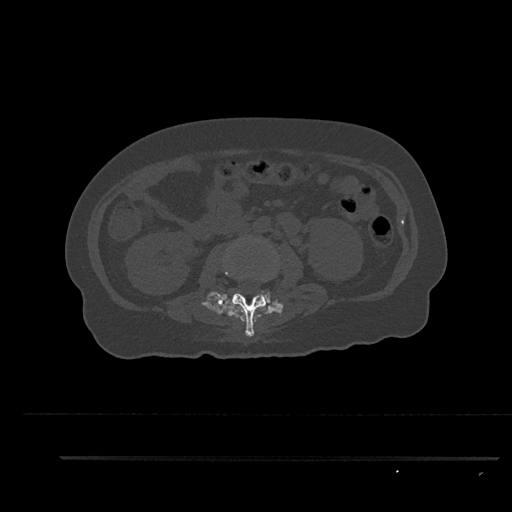
CT including the spine, one axial slice. Position 129 of 797 along the scan axis. Bone window (W 1800 / L 400 HU). 0.5 mm slice thickness. 512 × 512 image matrix, field of view 408 × 408 mm. Patient: female, 44 years. From the clinical record (not read from this slice): primary cancer: renal; vertebrae with lytic lesions (as recorded): L1.
Structures marked on this image (semi-automatically segmented with operator editing):
- L2 vertebra: bounding box [x1, y1, x2, y2] px = [224, 268, 268, 337]
- L3 vertebra: [225, 291, 278, 304]